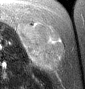
MRI of an extremity soft-tissue mass, one axial slice; position 22 of 46 along the scan axis; T2-weighted fat-saturated; MR volume resampled by the dataset authors to the PET/CT grid (not the native acquisition matrix); 3.27 mm slice thickness; 85 × 89 image matrix, field of view 83 × 87 mm. Female patient. From the clinical record (not read from this slice): histological type: leiomyosarcoma; grade: intermediate; site of the primary tumour: parascapusular.
Structures marked on this image (expert contour drawn on MRI and transferred to this co-registered scan by the dataset authors):
- gross tumour volume including surrounding oedema: box from (x=18, y=23) to (x=64, y=70) px
- gross tumour volume (mass): (x=18, y=23)–(x=64, y=70)